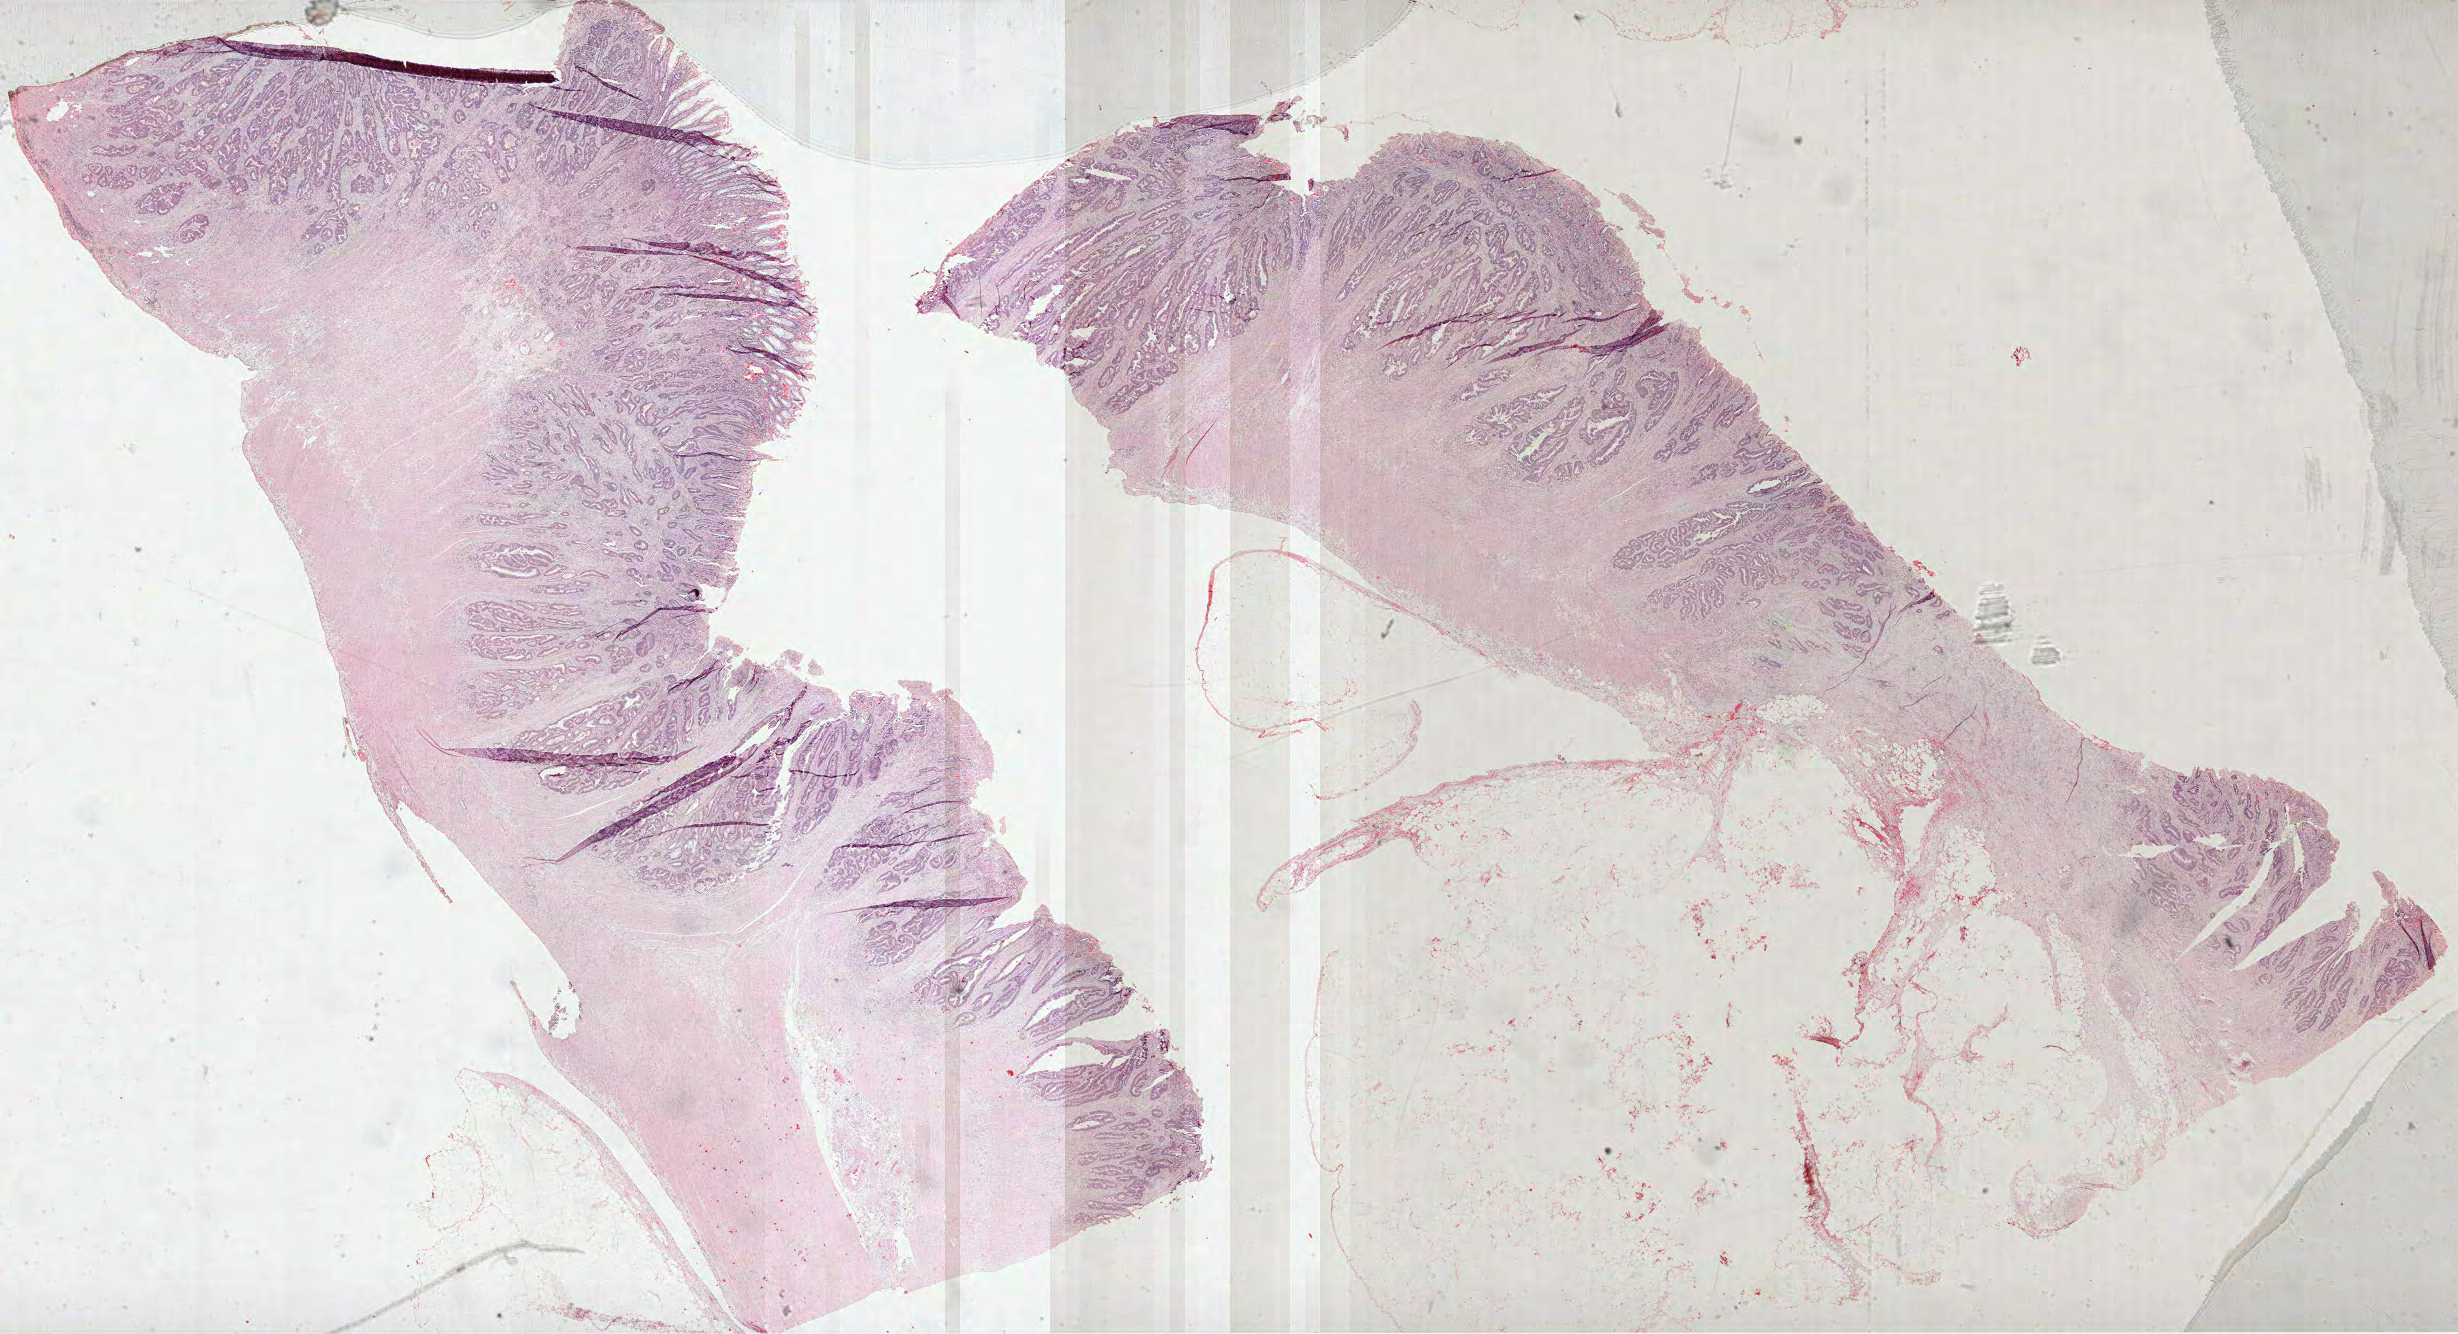
H&E-stained whole-slide image, a low-resolution overview of the entire scanned area, about 39.6 x 21.5 mm, FFPE section, sample: primary tumour, colon. Male patient; age at initial diagnosis 43 years.
AJCC pathologic stage: II (5th edition). Diagnosis: Adenocarcinoma, NOS (descending colon).